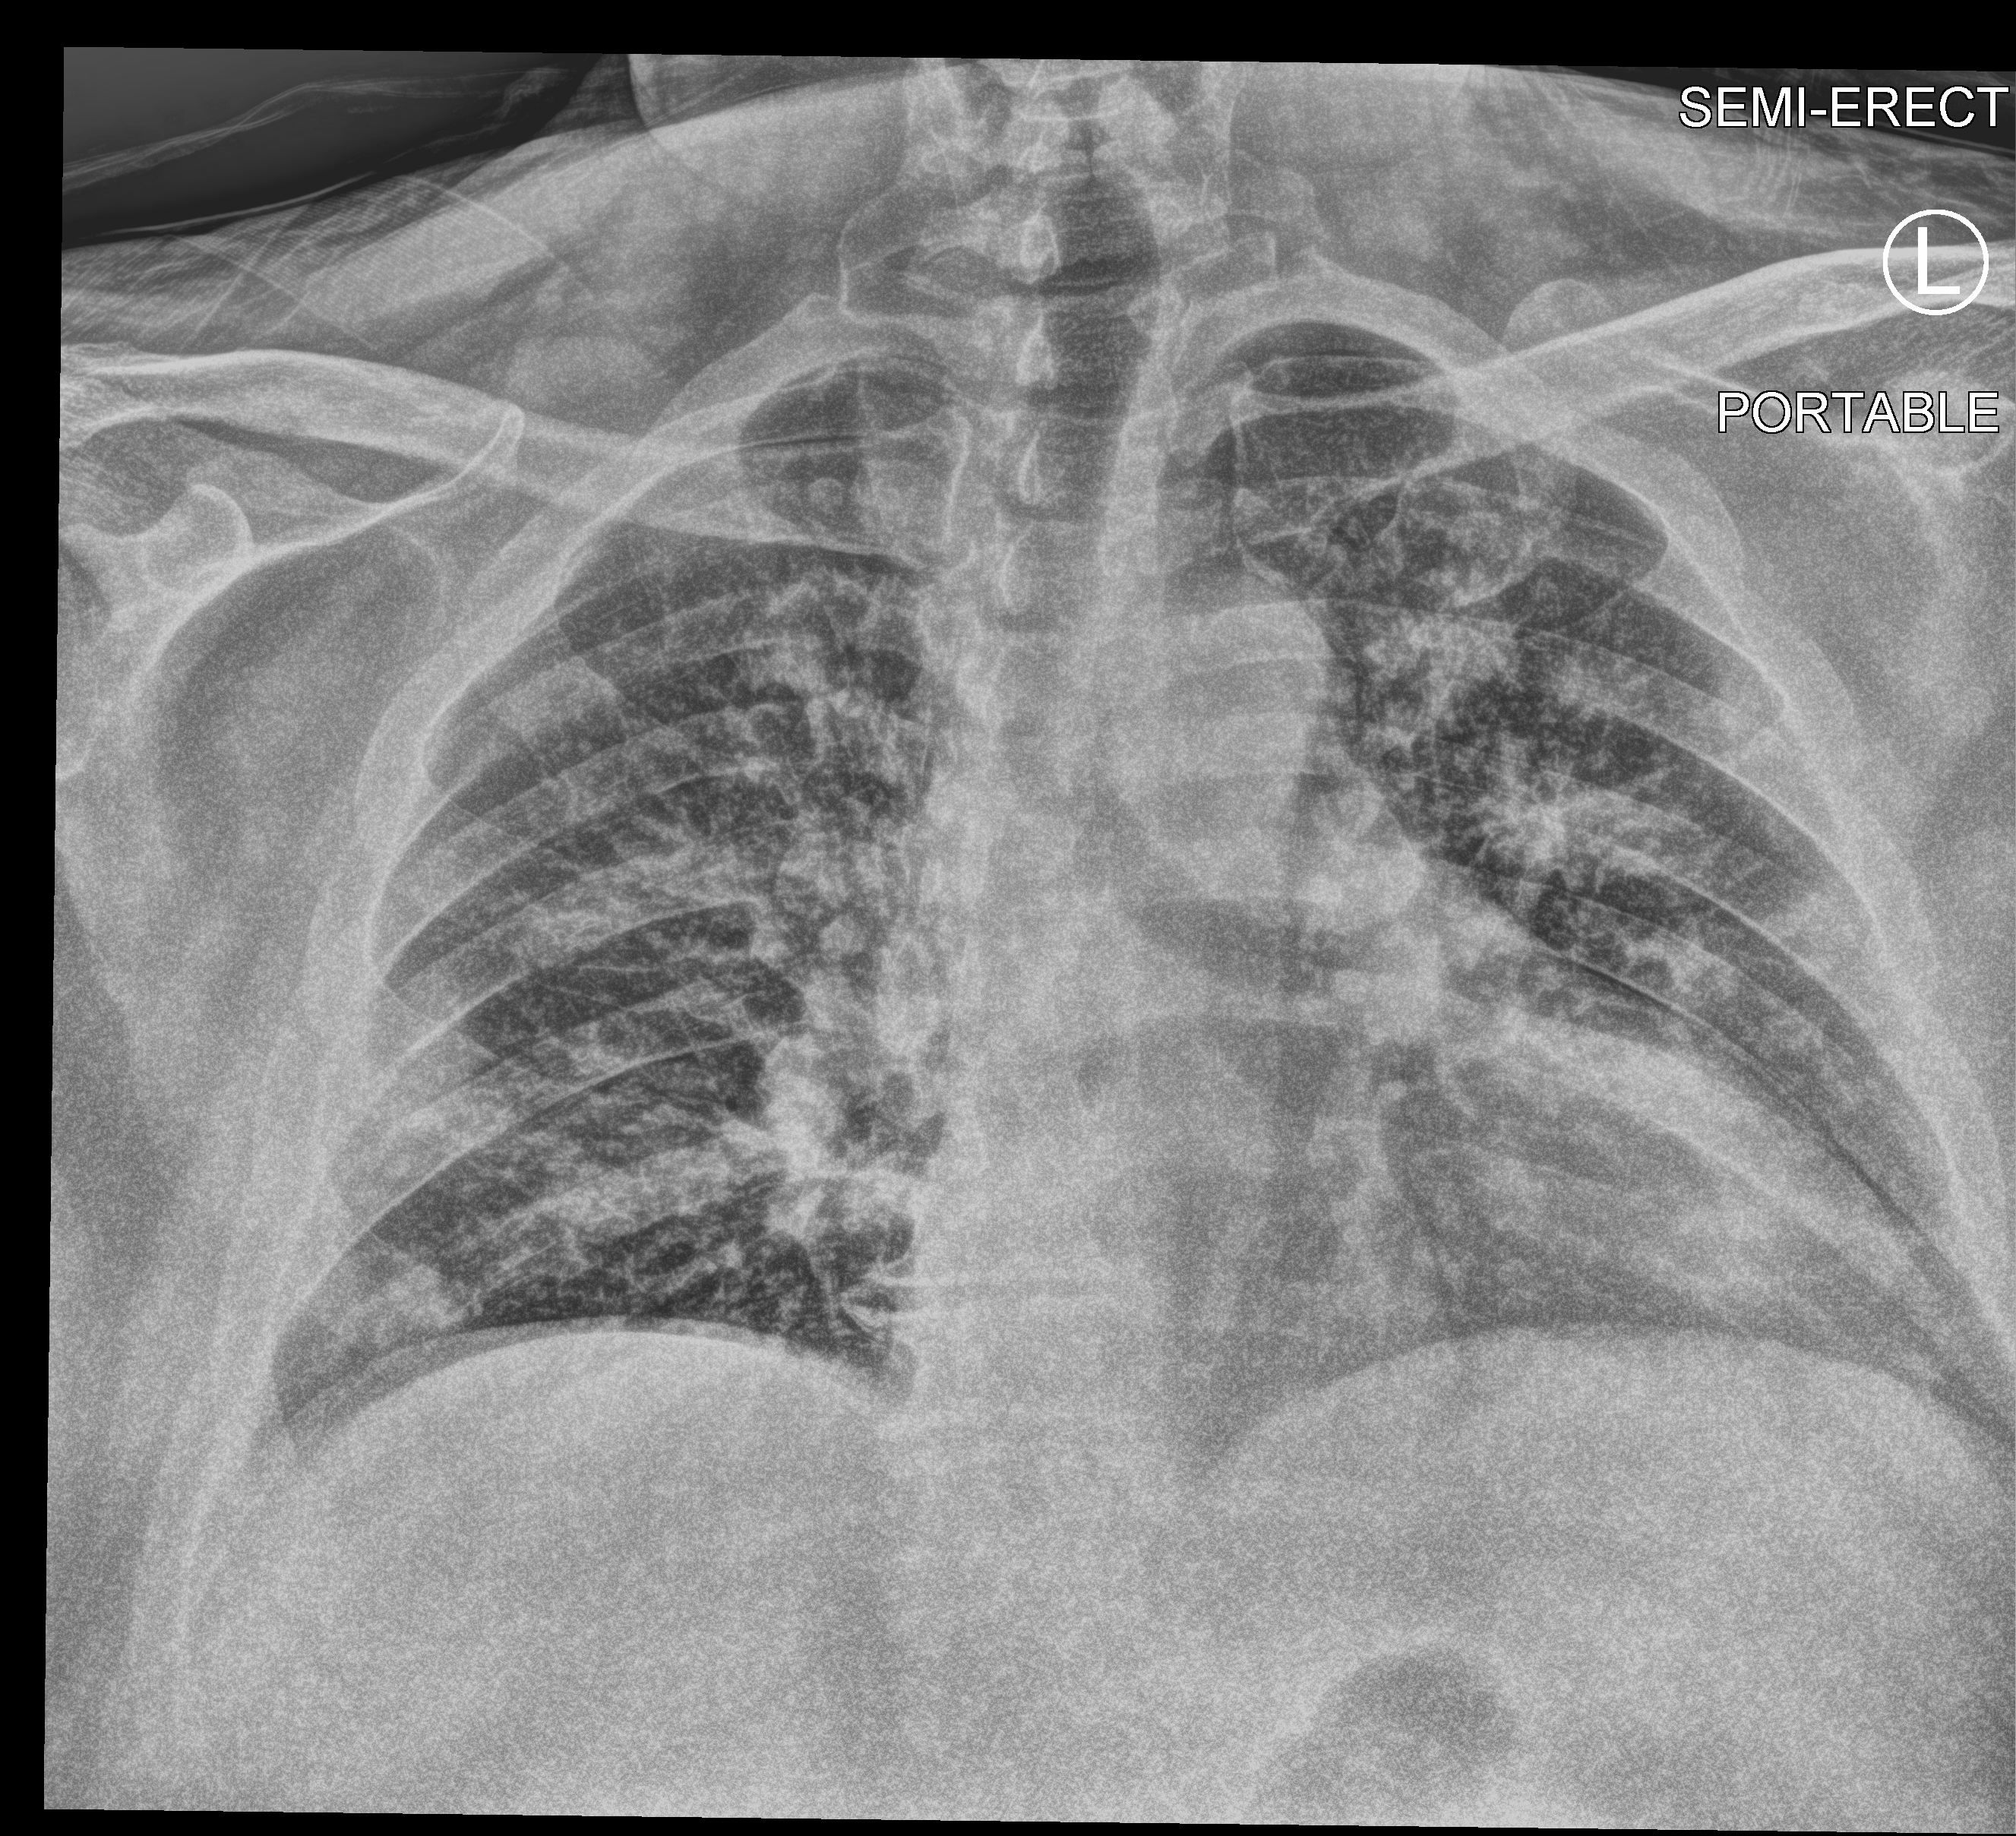
Chest X-ray (portable); anteroposterior (AP) projection. Patient hospitalised with COVID-19; male, aged 18–59 years.
Admission-level facts for this patient (not findings on this image; timing relative to this image not recorded): mechanically ventilated during this hospital stay: no.